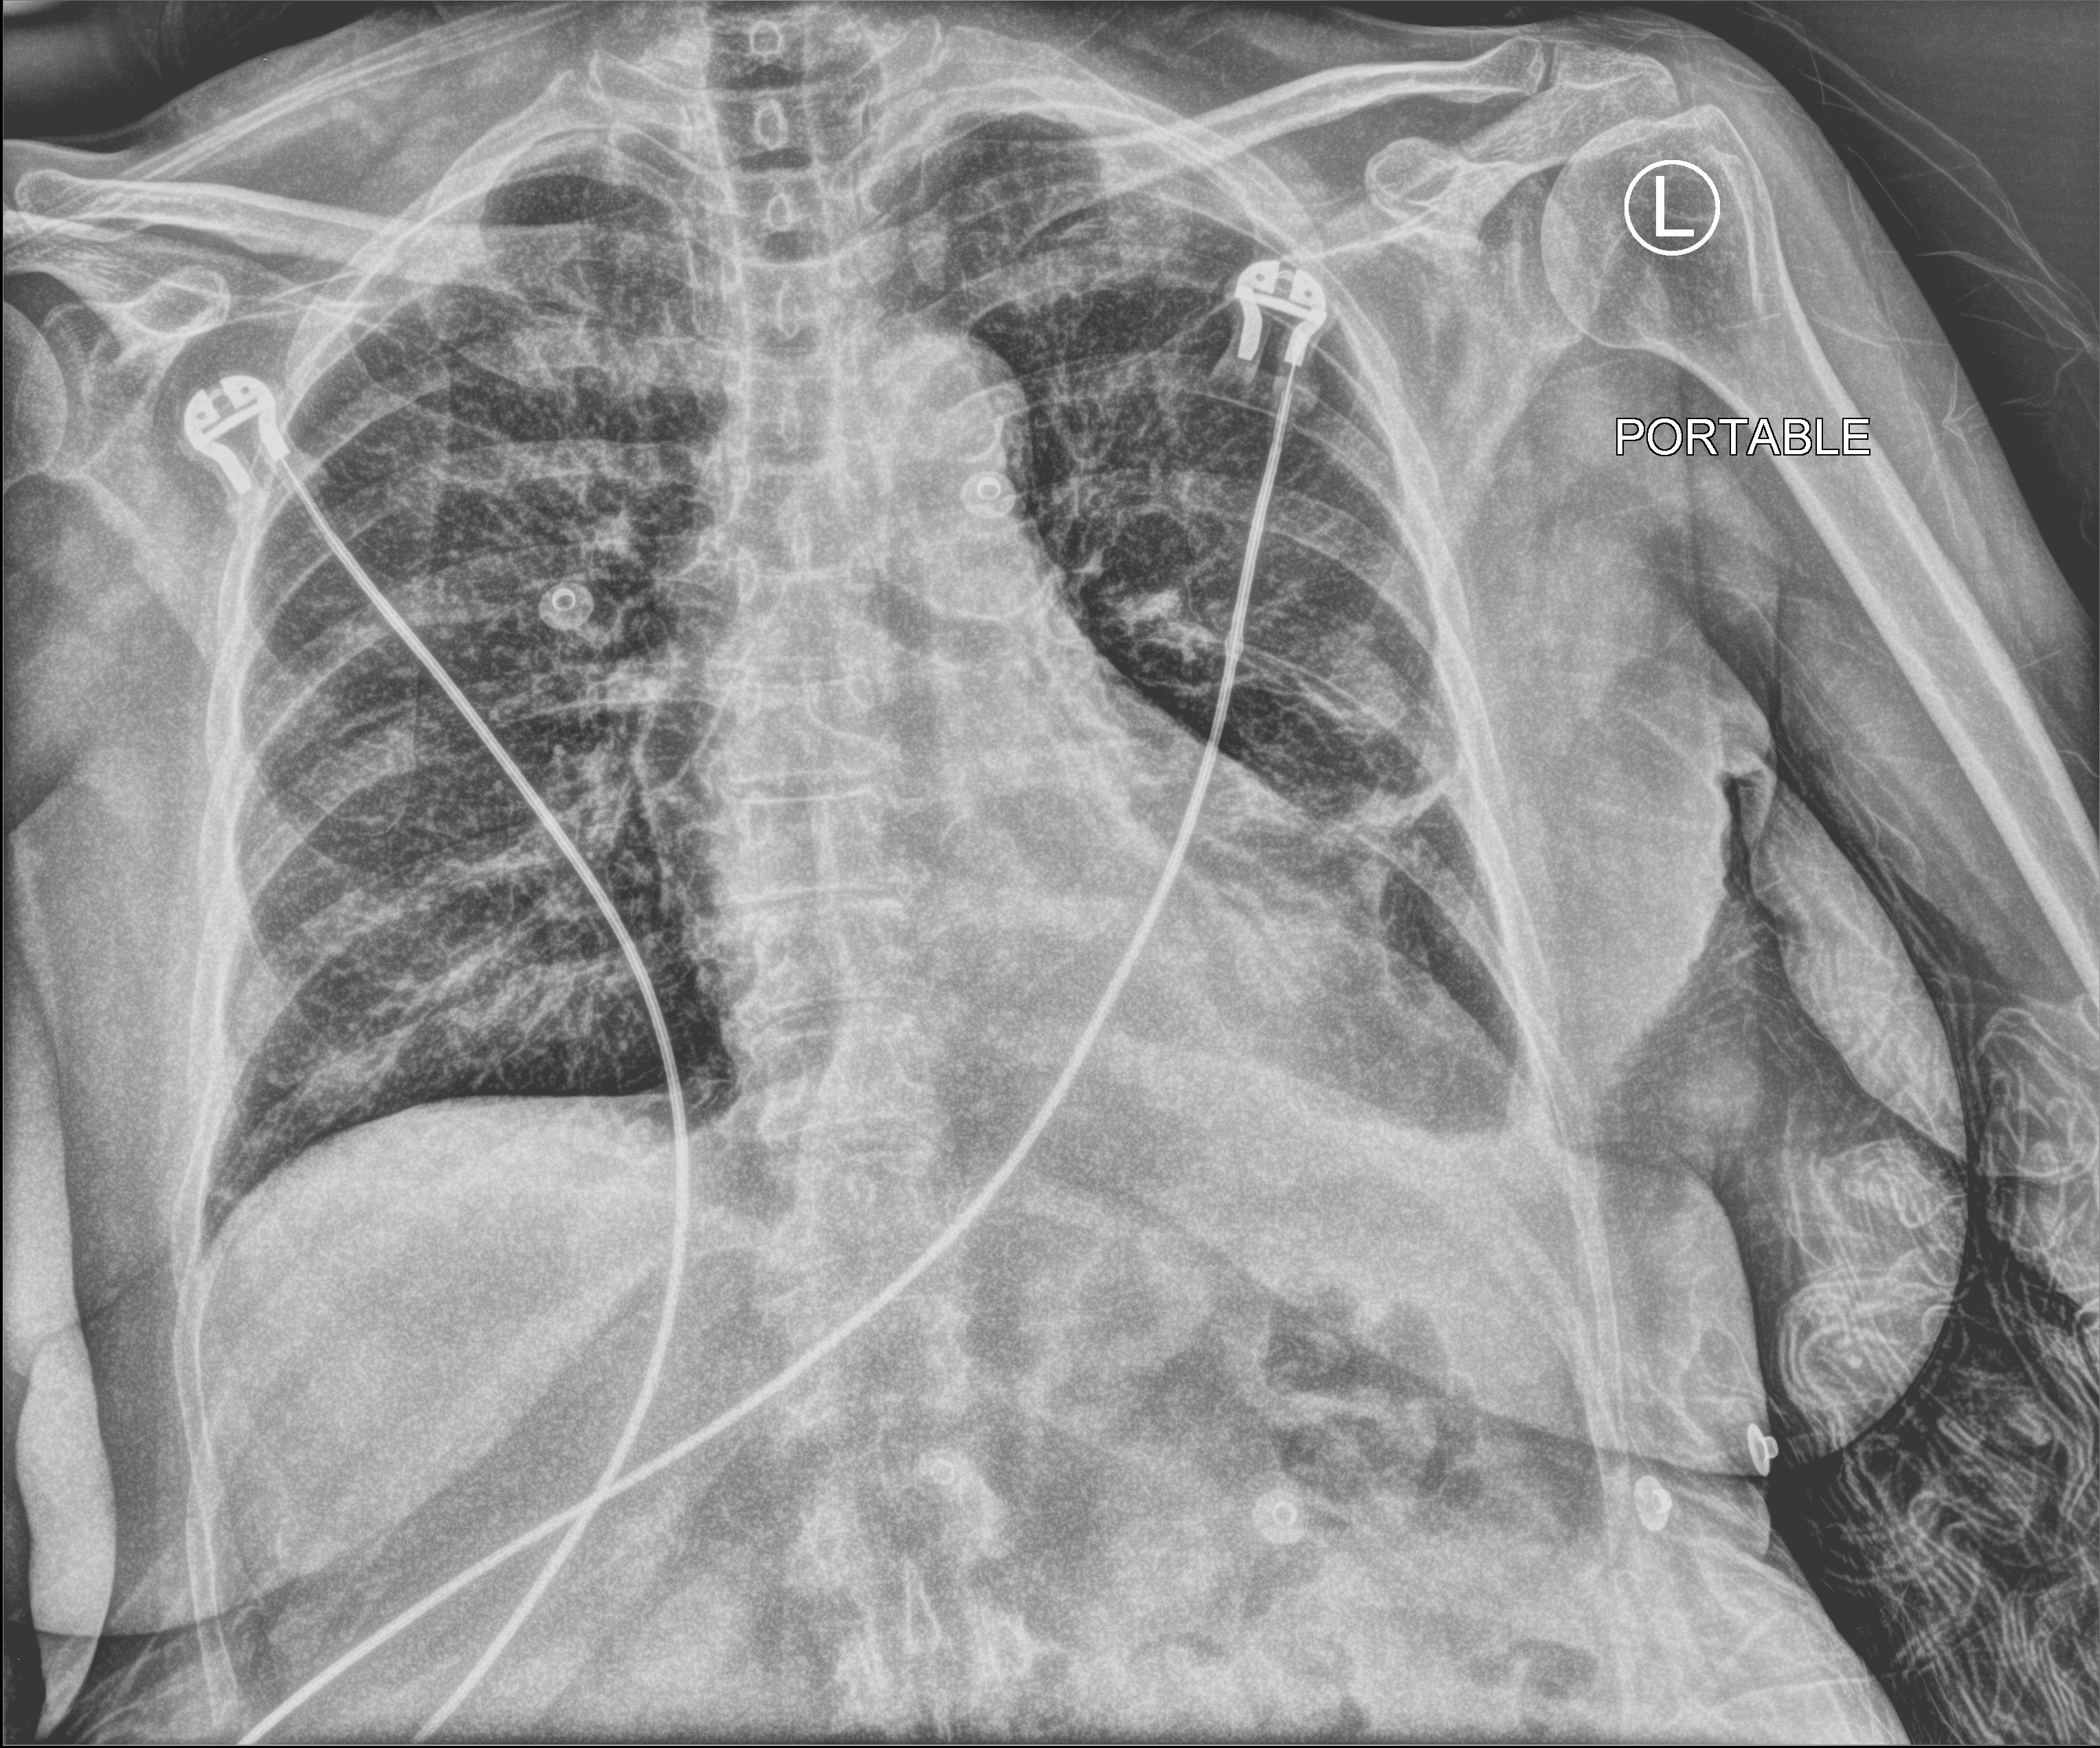
Portable chest radiograph; anteroposterior (AP) projection. Patient hospitalised with COVID-19; female, aged 75–90 years.
Hospital-stay facts (about this admission, not read from this image; timing relative to this image not recorded): admitted to intensive care during this hospital stay: no; length of hospital stay: 21 days; mechanically ventilated during this hospital stay: no.